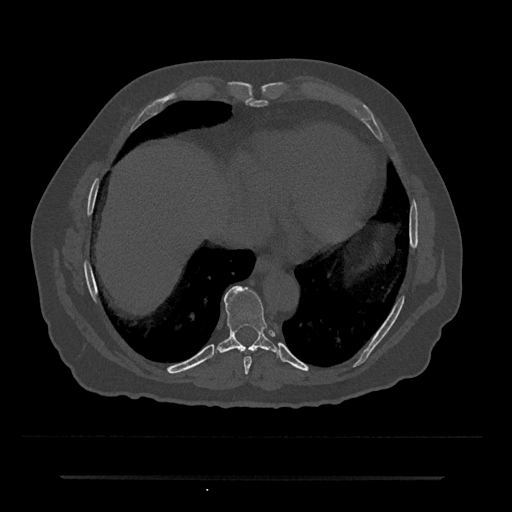
CT including the spine, one axial slice; slice 290 of 797 in the series (ordered by position); reconstruction kernel Br40s/3; 120 kVp; bone window (W 1800 / L 400 HU); 0.5 mm slice thickness; 512 × 512 image matrix, field of view 437 × 437 mm. Male patient, age 69 years. Case-level facts recorded for this patient, not image findings: primary cancer: prostate.
Outlined on this slice (semi-automatically segmented with operator editing):
- T8 vertebra: box from (x=244, y=356) to (x=252, y=374) px
- T9 vertebra: (x=216, y=286)–(x=278, y=354)